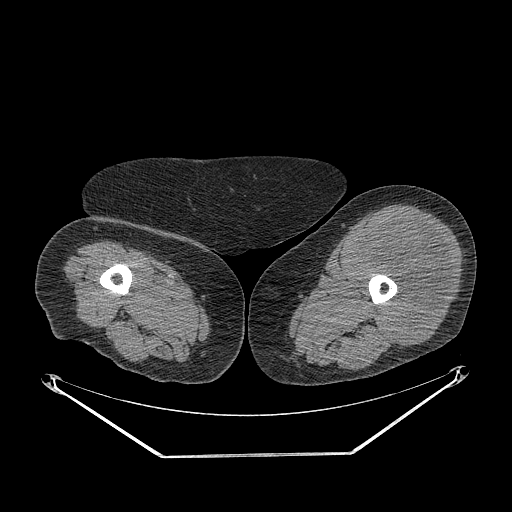
CT of an extremity soft-tissue mass (from a PET/CT study), one axial slice. Slice 229 of 267 in the series (ordered by position). Reconstruction kernel STANDARD. Soft-tissue window (W 400 / L 40 HU). 512 × 512 image matrix, field of view 500 × 500 mm. Female patient. From the clinical record (not read from this slice): histological type: undifferentiated – high grade; grade: high; site of the primary tumour: left thigh.
Structures marked on this image (expert contour drawn on MRI and transferred to this co-registered scan by the dataset authors):
- gross tumour volume including surrounding oedema: bounding box [x1, y1, x2, y2] px = [354, 215, 453, 346]
- gross tumour volume (mass): [354, 215, 451, 346]